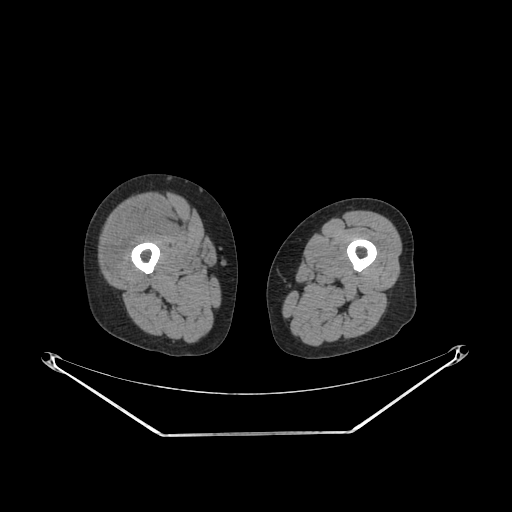
CT of an extremity soft-tissue mass (from a PET/CT study), one axial slice. Slice 226 of 311 in the series (ordered by position). Soft-tissue window (W 400 / L 40 HU). 512 × 512 image matrix, field of view 500 × 500 mm. Female patient. From the clinical record (not read from this slice): histological type: pleiomorphic undifferentiated sarcoma; grade: high; site of the primary tumour: right quadricep.
Annotated regions visible in this slice (expert contour drawn on MRI and transferred to this co-registered scan by the dataset authors):
- tumour plus oedema (research contour): bounding box (x1, y1, x2, y2) in pixels: (105, 203, 168, 275)